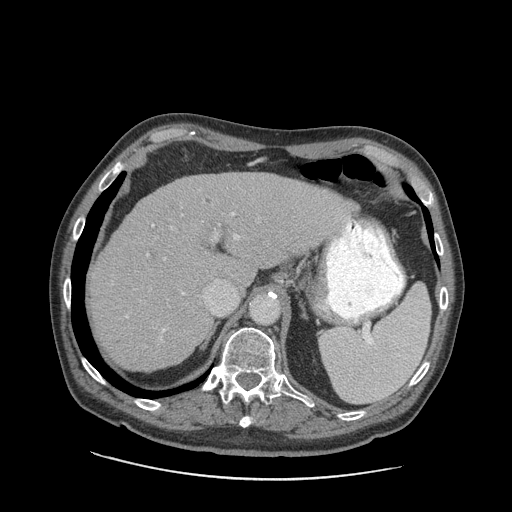
Contrast-enhanced abdominal CT (liver protocol), one axial slice; slice 63 of 89 in the series (ordered by position); reconstruction kernel STANDARD; soft-tissue window (W 400 / L 40 HU); 512 × 512 image matrix, field of view 420 × 420 mm. From the clinical record (not read from this slice): diagnosis: hepatocellular carcinoma (patient treated with transarterial chemoembolisation; whether this scan precedes or follows treatment is not stated here); TNM stage (as recorded): Stage-I; Child-Pugh class: A; tumour differentiation: moderately differentiated; tumour nodularity: uninodular.
Annotated regions visible in this slice (semi-automatically segmented with operator editing):
- liver parenchyma outside the tumour (the mass and vessels are separate outlines, so this box may not span the whole liver): bounding box (x1, y1, x2, y2) in pixels: (91, 172, 354, 372)
- liver vessels: (126, 189, 351, 342)